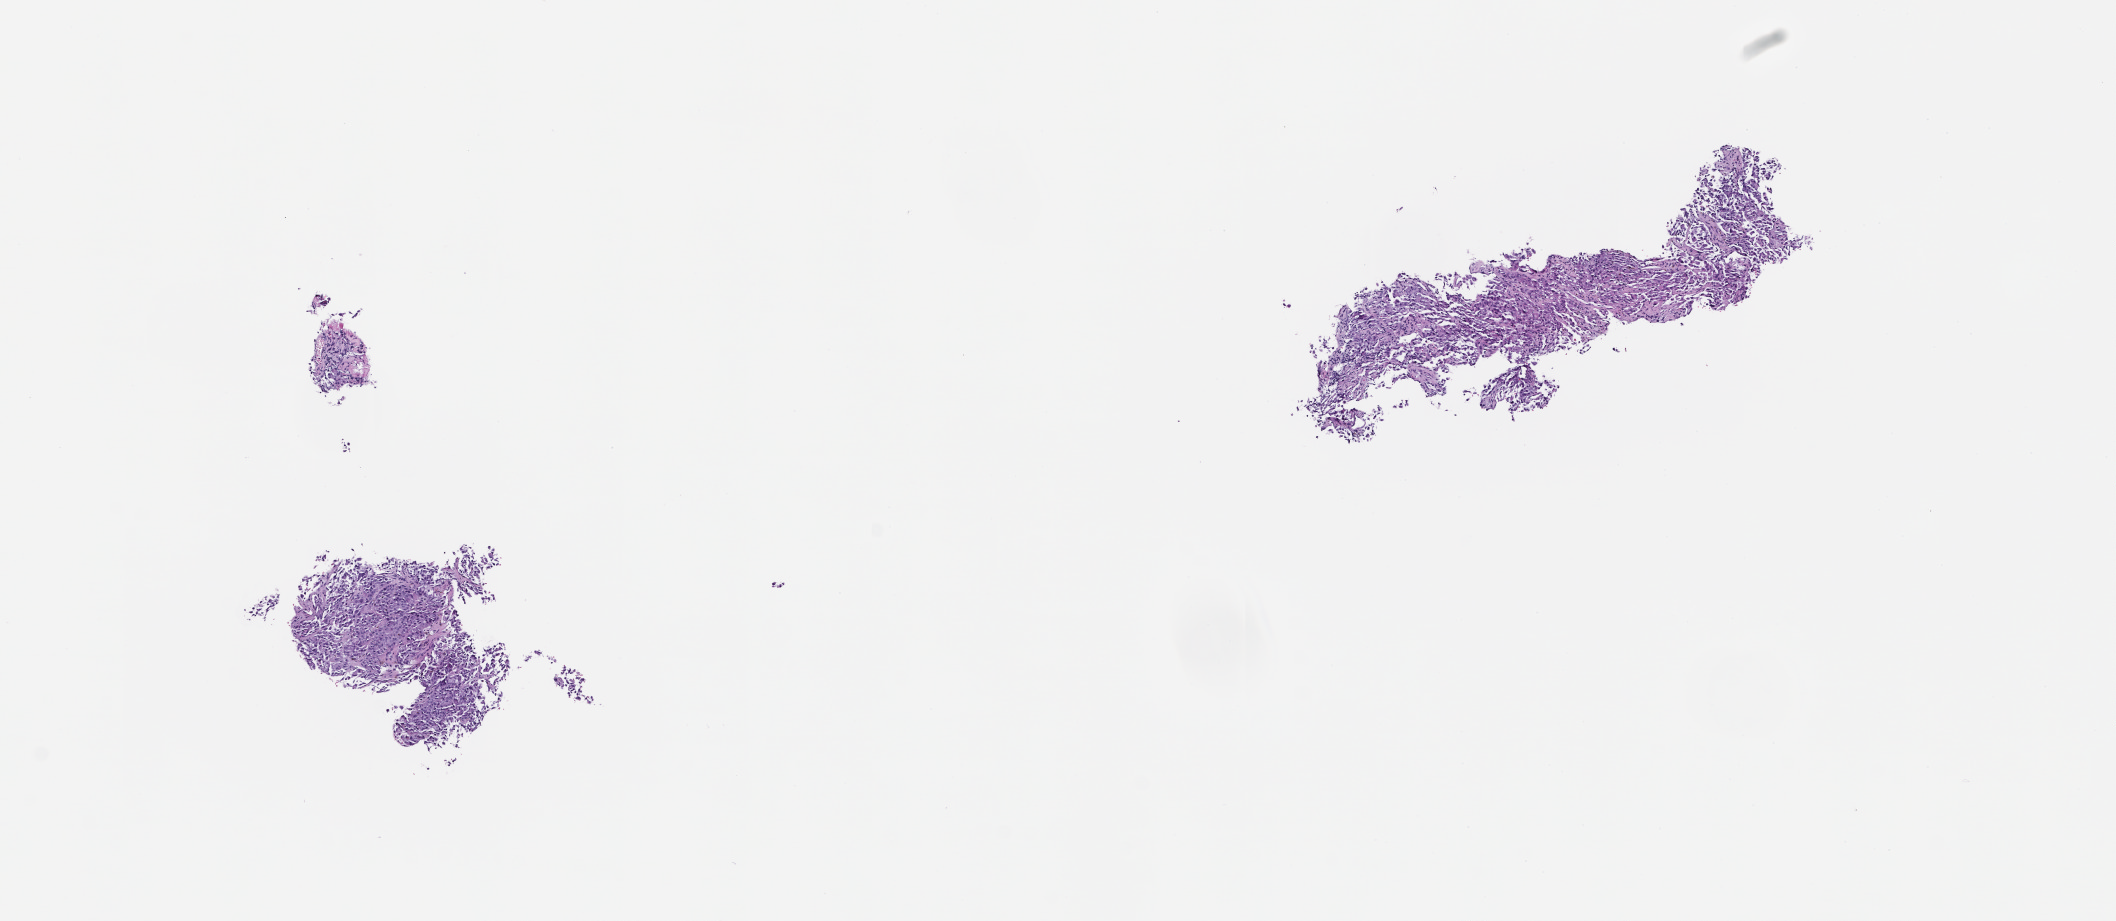
Digitized hematoxylin and eosin (H&E)-stained section — a low-resolution overview of the entire scanned area, about 8.5 x 3.7 mm. Formalin-fixed, paraffin-embedded (FFPE) tissue. Patient sex: male.
• this section: metastasis (sampled organ not recorded)
• patient diagnosis (primary): Melanoma